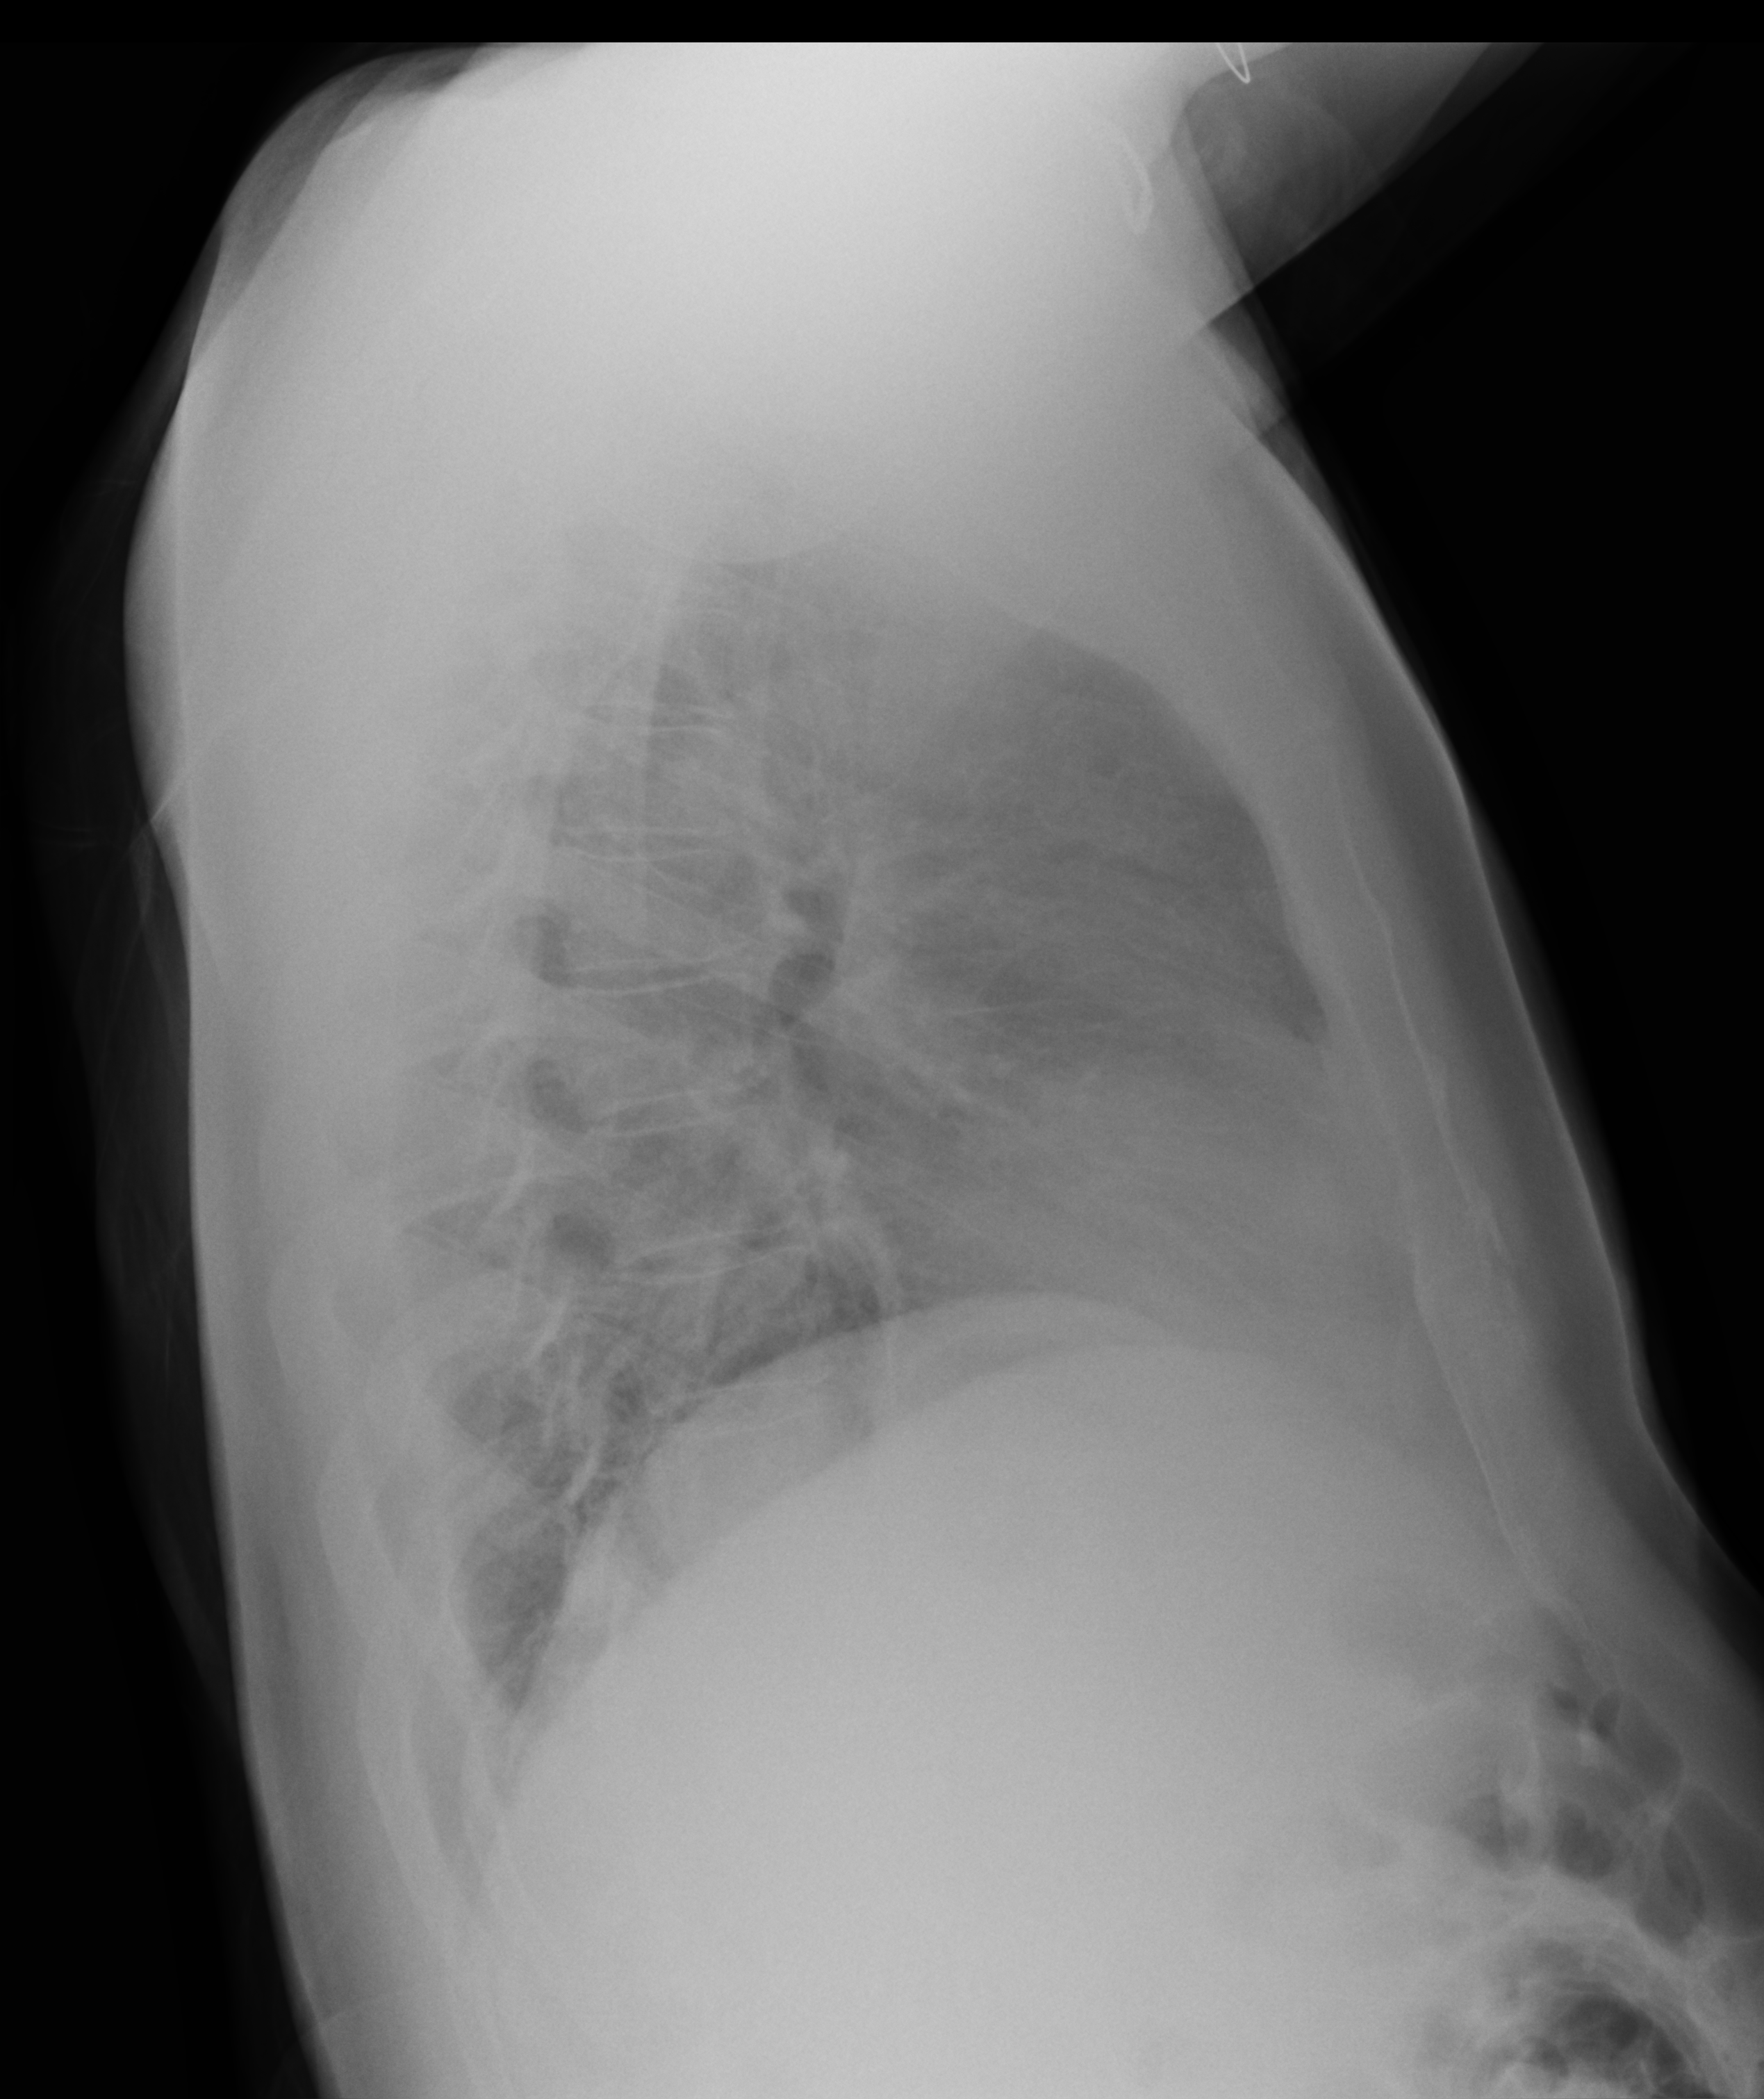
Portable chest radiograph; lateral projection. Patient hospitalised with COVID-19; male, aged 60–74 years.
Admission-level facts for this patient (not findings on this image; timing relative to this image not recorded): mechanically ventilated during this hospital stay: no; admitted to intensive care during this hospital stay: no.